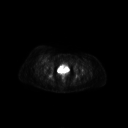
FDG PET of an extremity soft-tissue mass (from a PET/CT study), one axial slice. Slice 69 of 267 in the series (ordered by position). 3.27 mm slice thickness. 128 × 128 image matrix, field of view 700 × 700 mm. Patient: female, 56 years. From the clinical record (not read from this slice): histological type: malignant solitary fibrous tumor; grade: intermediate; site of the primary tumour: right thigh.
Annotated regions visible in this slice (expert contour drawn on MRI and transferred to this co-registered scan by the dataset authors):
- gross tumour volume including surrounding oedema: bounding box <38,56,47,62> (left, top, right, bottom; pixels)